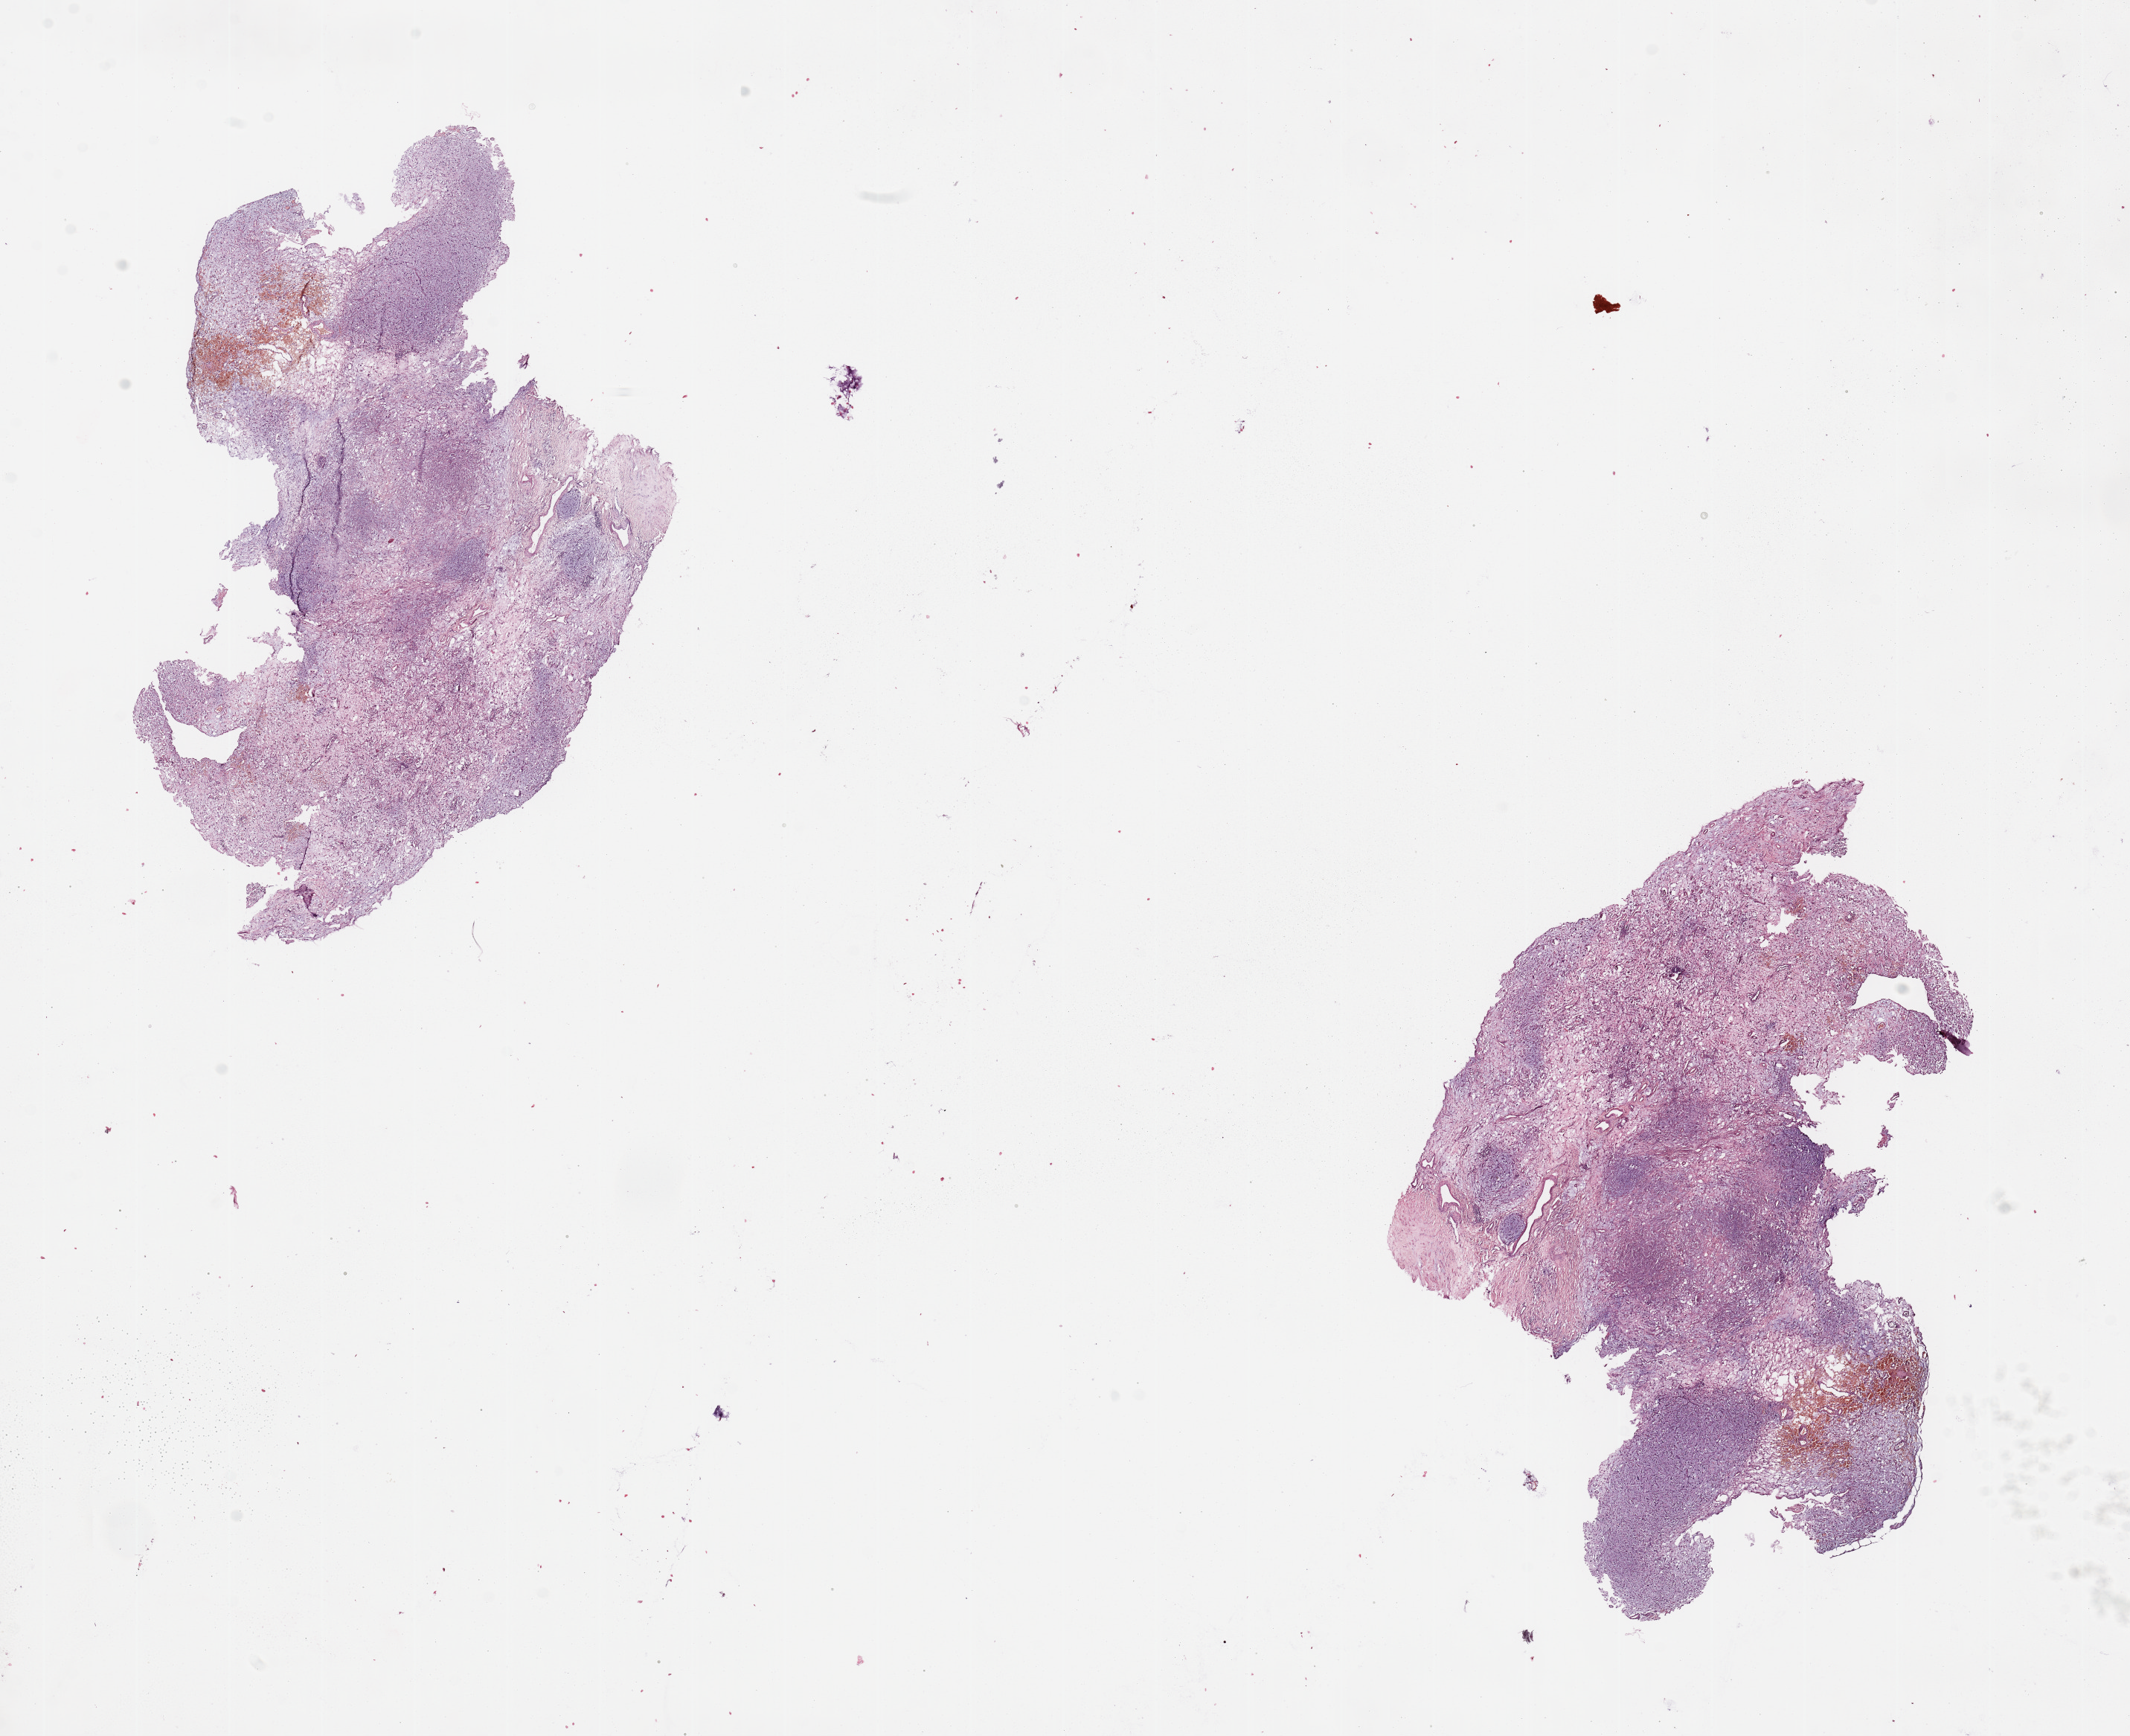
Whole-slide histology image, Hematoxylin and eosin (H&E) stained, a low-resolution overview of the entire scanned area, about 22.6 x 18.5 mm (acquisition: 20x scan). 20-year-old male patient.
* patient diagnosis (cohort enrolment): sarcoma (site not recorded at cohort level)